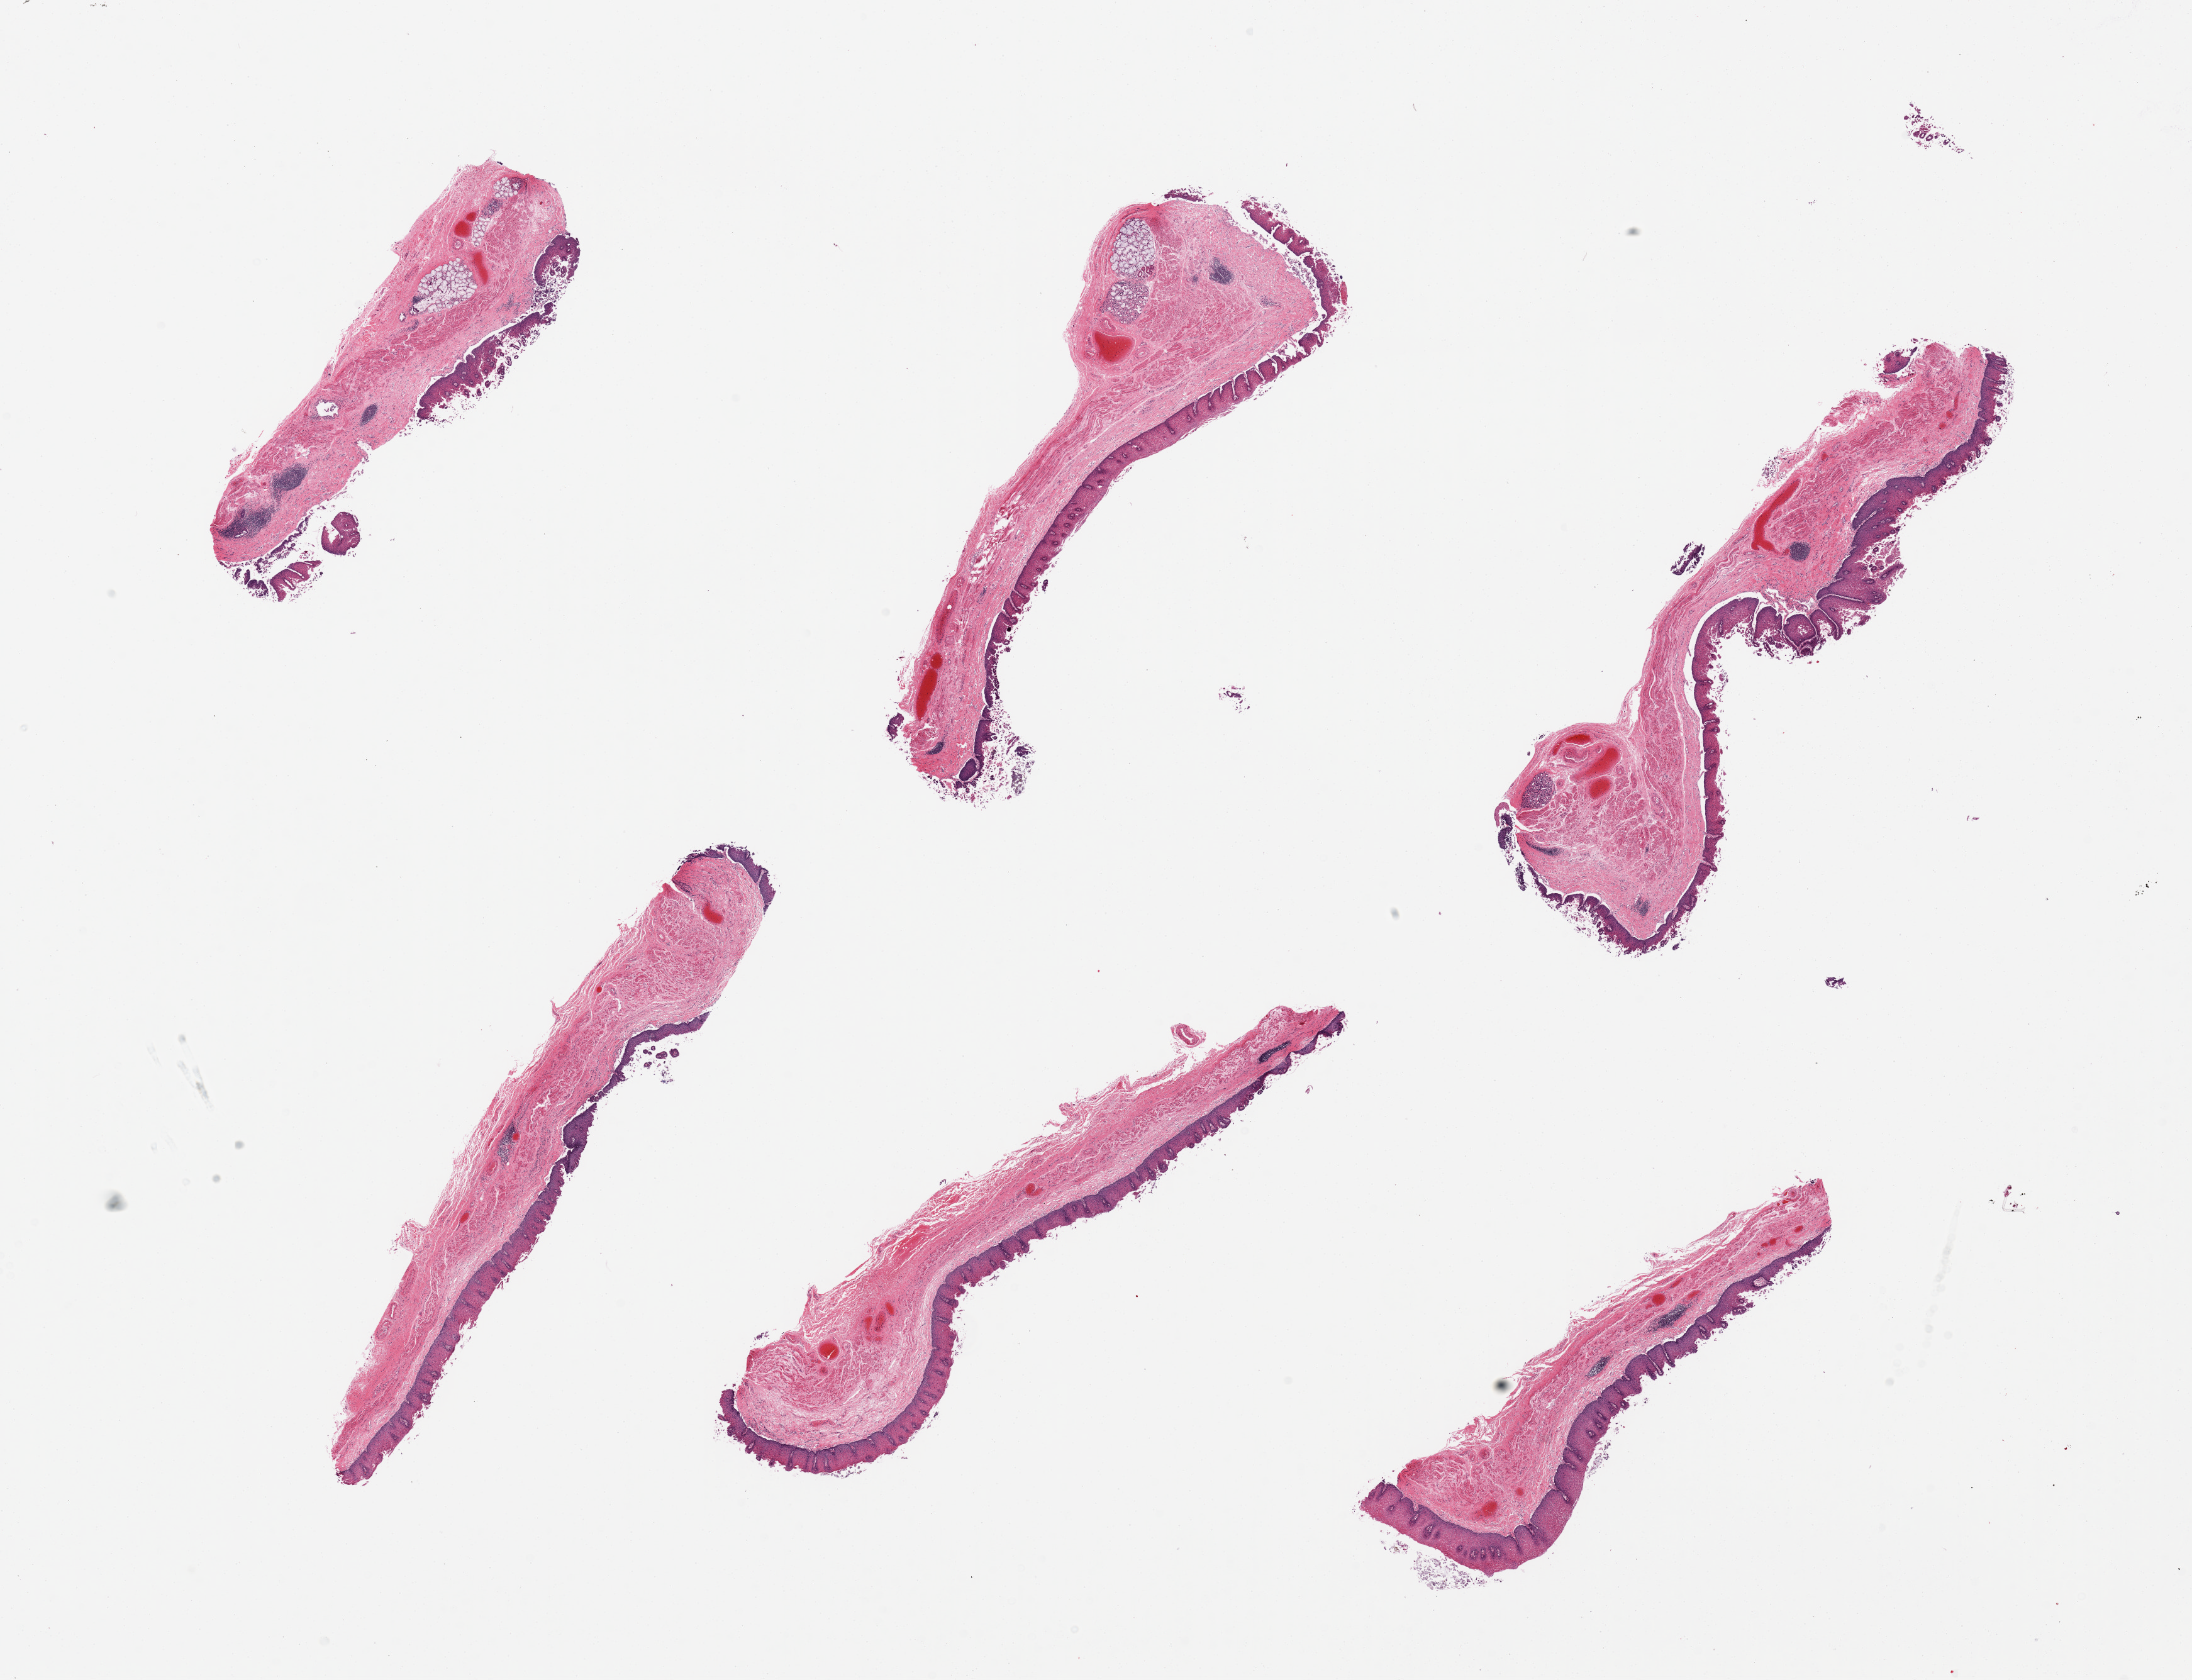
Digitized hematoxylin and eosin (H&E)-stained section, shown as a low-resolution overview of the whole scanned area (about 27.6 x 21.1 mm, slide scanned at 20x), PAXgene-fixed paraffin-embedded (PFPE) section, target tissue: esophageal mucous membrane, tissue donor sample. Donor sex: male.
• review note (as recorded): 6 pieces, epithelium partially sloughing, few submucosal glands (some)